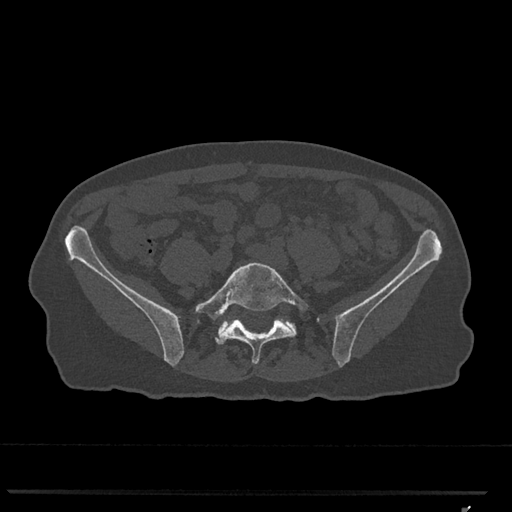
CT including the spine, one axial slice. Position 145 of 793 along the scan axis. 120 kVp. Bone window (W 1800 / L 400 HU). 0.5 mm slice thickness. 512 × 512 image matrix, field of view 380 × 380 mm. Patient: female, 62 years. From the clinical record (not read from this slice): primary cancer: renal.
Structures marked on this image (semi-automatically segmented with operator editing):
- L5 vertebra: bounding box [x1, y1, x2, y2] px = [195, 262, 309, 364]